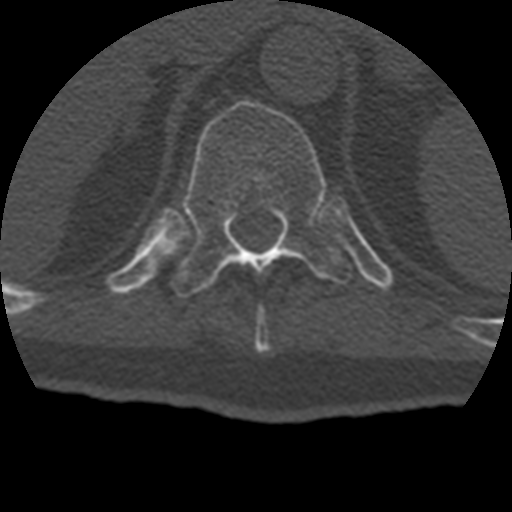
CT including the spine, one axial slice; position 201 of 399 along the scan axis; reconstruction kernel STANDARD; 120 kVp; bone window (W 1800 / L 400 HU); 1.25 mm slice thickness; 512 × 512 image matrix. Patient age 69 years. From the clinical record (not read from this slice): primary cancer: prostate.
Structures marked on this image (semi-automatically segmented with operator editing):
- T10 vertebra: bounding box (x1, y1, x2, y2) in pixels: (255, 311, 269, 352)
- T11 vertebra: (173, 100, 353, 297)